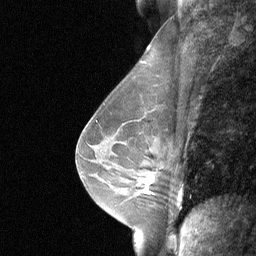
Breast MRI (dynamic contrast-enhanced), one sagittal slice. Slice 41 of 64 in the series (ordered by position). Dynamic contrast-enhanced study with each time point stored as its own series, time point 2 of 3 at this slice position (early post-contrast, ordered by acquisition time). 1.5 T. TE 4.8 ms, TR 27 ms. 2 mm slice thickness. 256 × 256 image matrix, field of view 200 × 200 mm. Patient: female, 48 years. Case-level facts recorded for this patient, not image findings: setting: breast cancer imaged before/during neoadjuvant chemotherapy; receptor status: HR-positive, HER2-negative.
Structures marked on this image (semi-automatically segmented with operator editing):
- analysis volume of interest (the breast-tissue region the enhancement analysis was run in; not a lesion): bounding box [x1, y1, x2, y2] px = [131, 165, 164, 200]
- tumour enhancement mask (voxels above the 90 % enhancement threshold inside the analysis volume of interest): [142, 179, 148, 193]